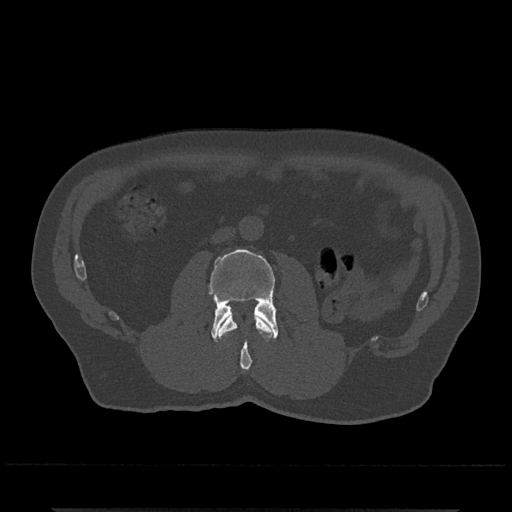
CT including the spine, one axial slice. Position 246 of 797 along the scan axis. Reconstruction kernel Br40s/3. 120 kVp. Bone window (W 1800 / L 400 HU). 0.5 mm slice thickness. 512 × 512 image matrix, field of view 393 × 393 mm. Male patient, age 67 years. From the clinical record (not read from this slice): primary cancer: prostate.
Annotated regions visible in this slice (semi-automatically segmented with operator editing):
- L2 vertebra: bounding box <218,315,272,371> (left, top, right, bottom; pixels)
- L3 vertebra: <208,249,279,341>